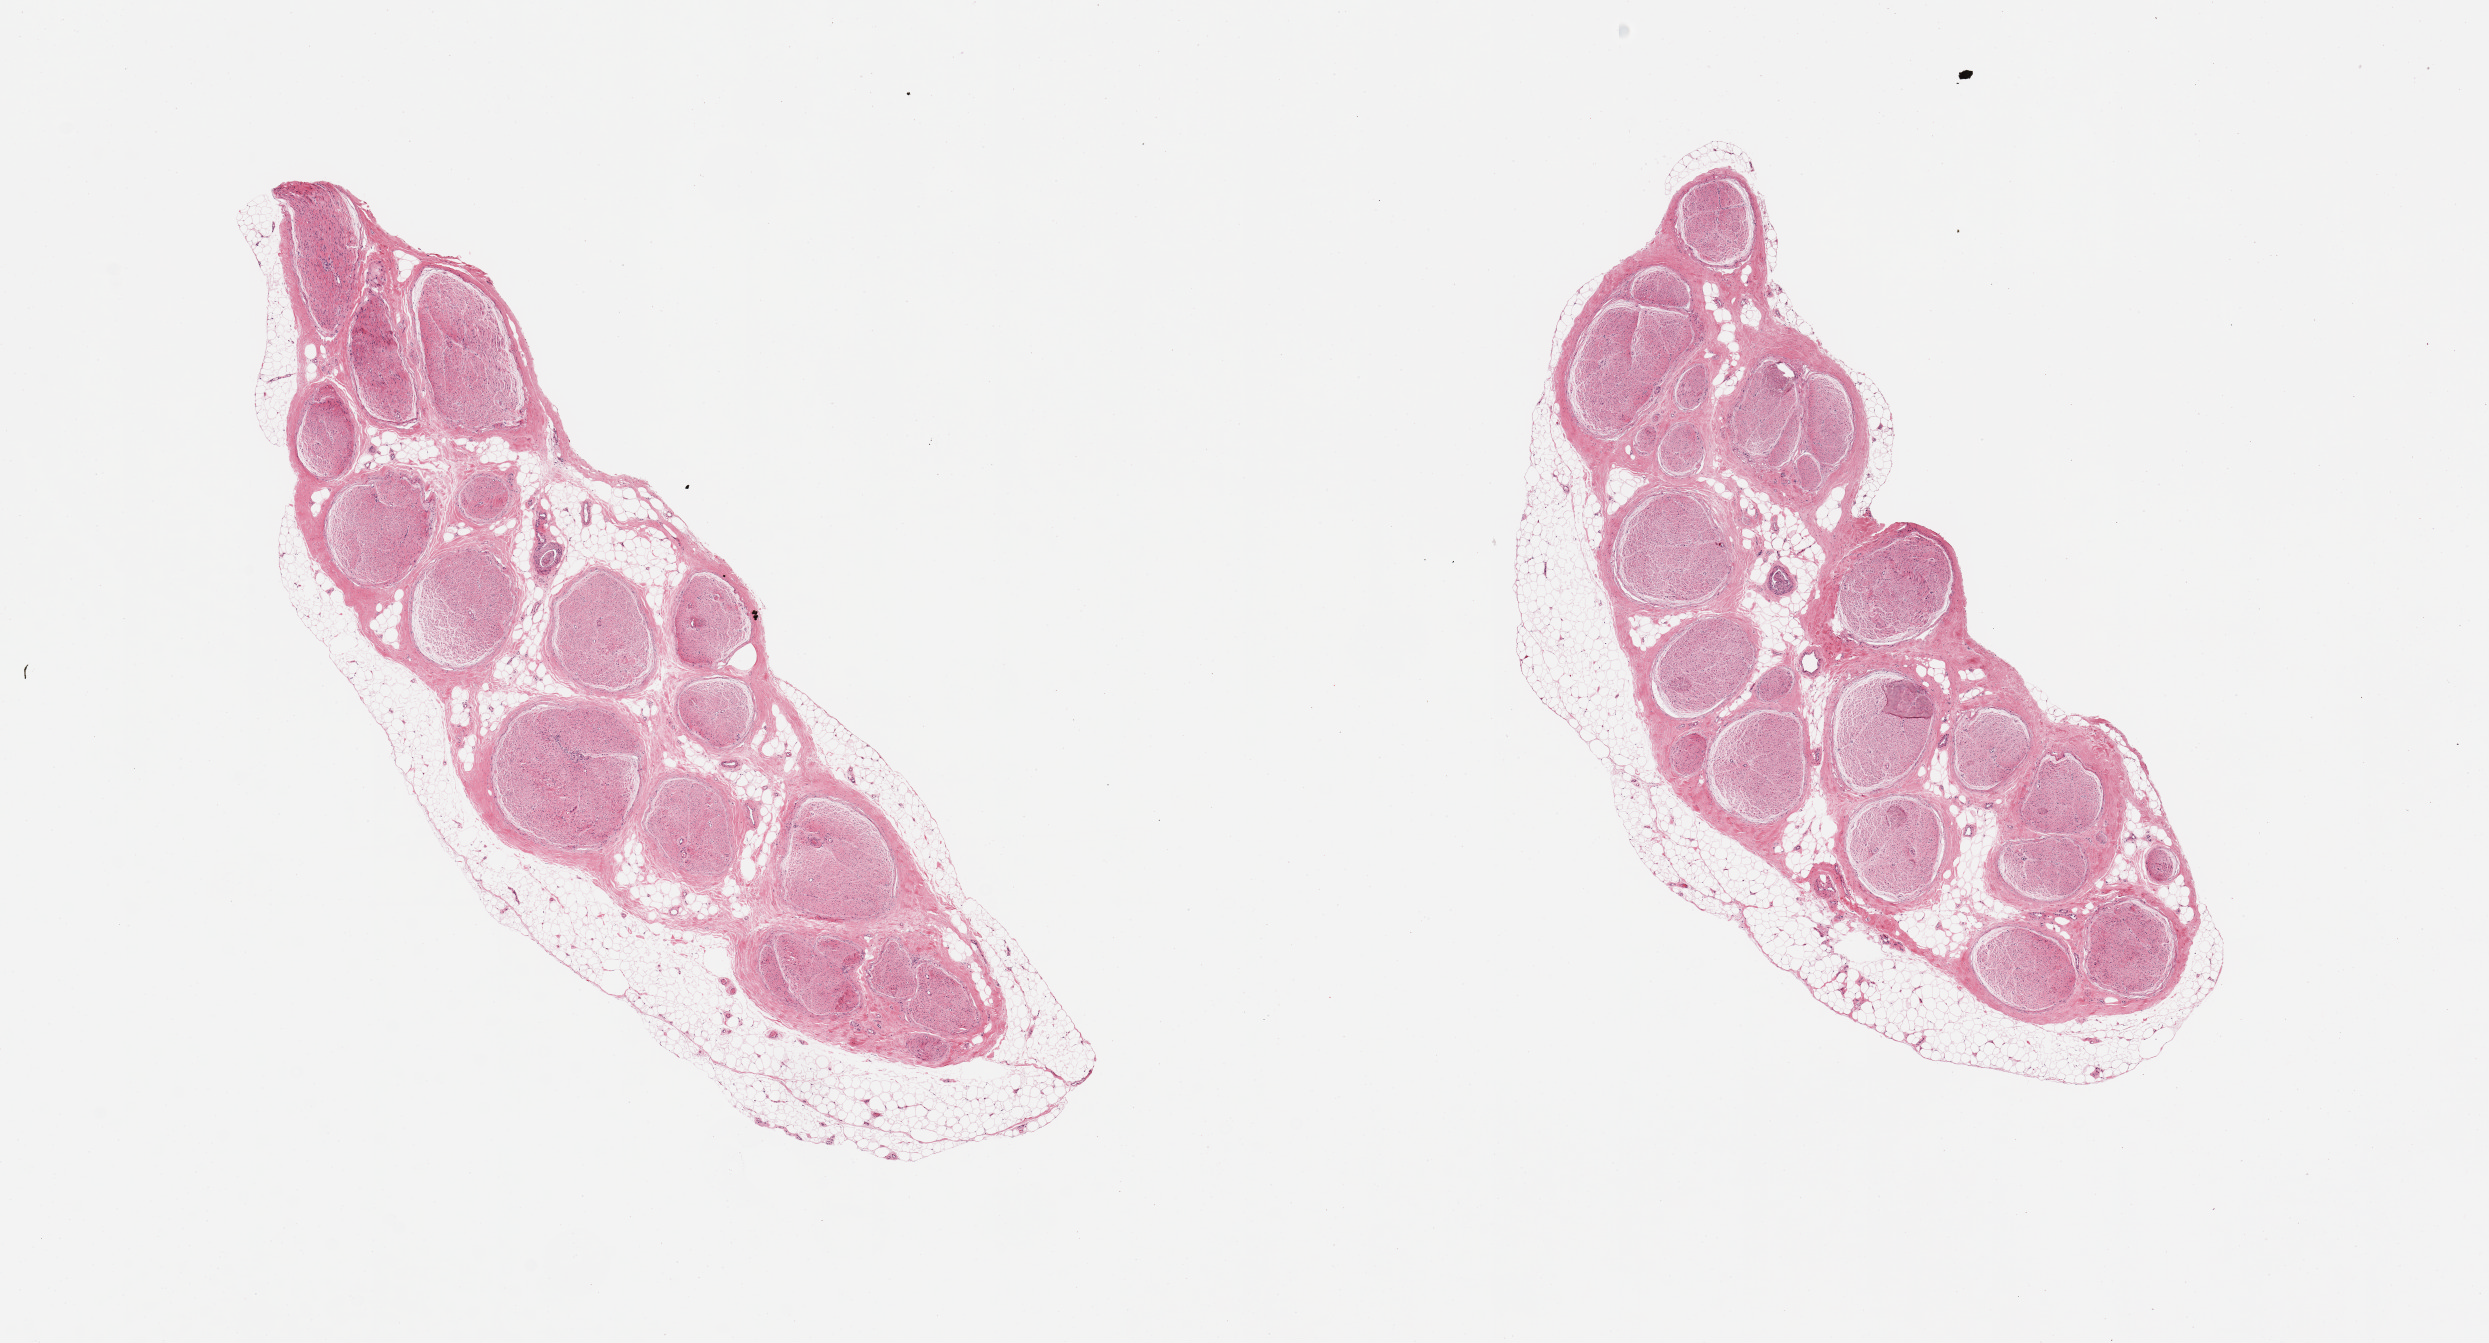
Whole-slide image, haematoxylin and eosin stain, a low-resolution overview of the entire scanned area, about 19.7 x 10.6 mm; PAXgene-fixed, paraffin-embedded tissue; target tissue: tibial nerve; tissue donor sample.
Pathologist's review note for this sample: 2 pieces. 20% external and internal fat.